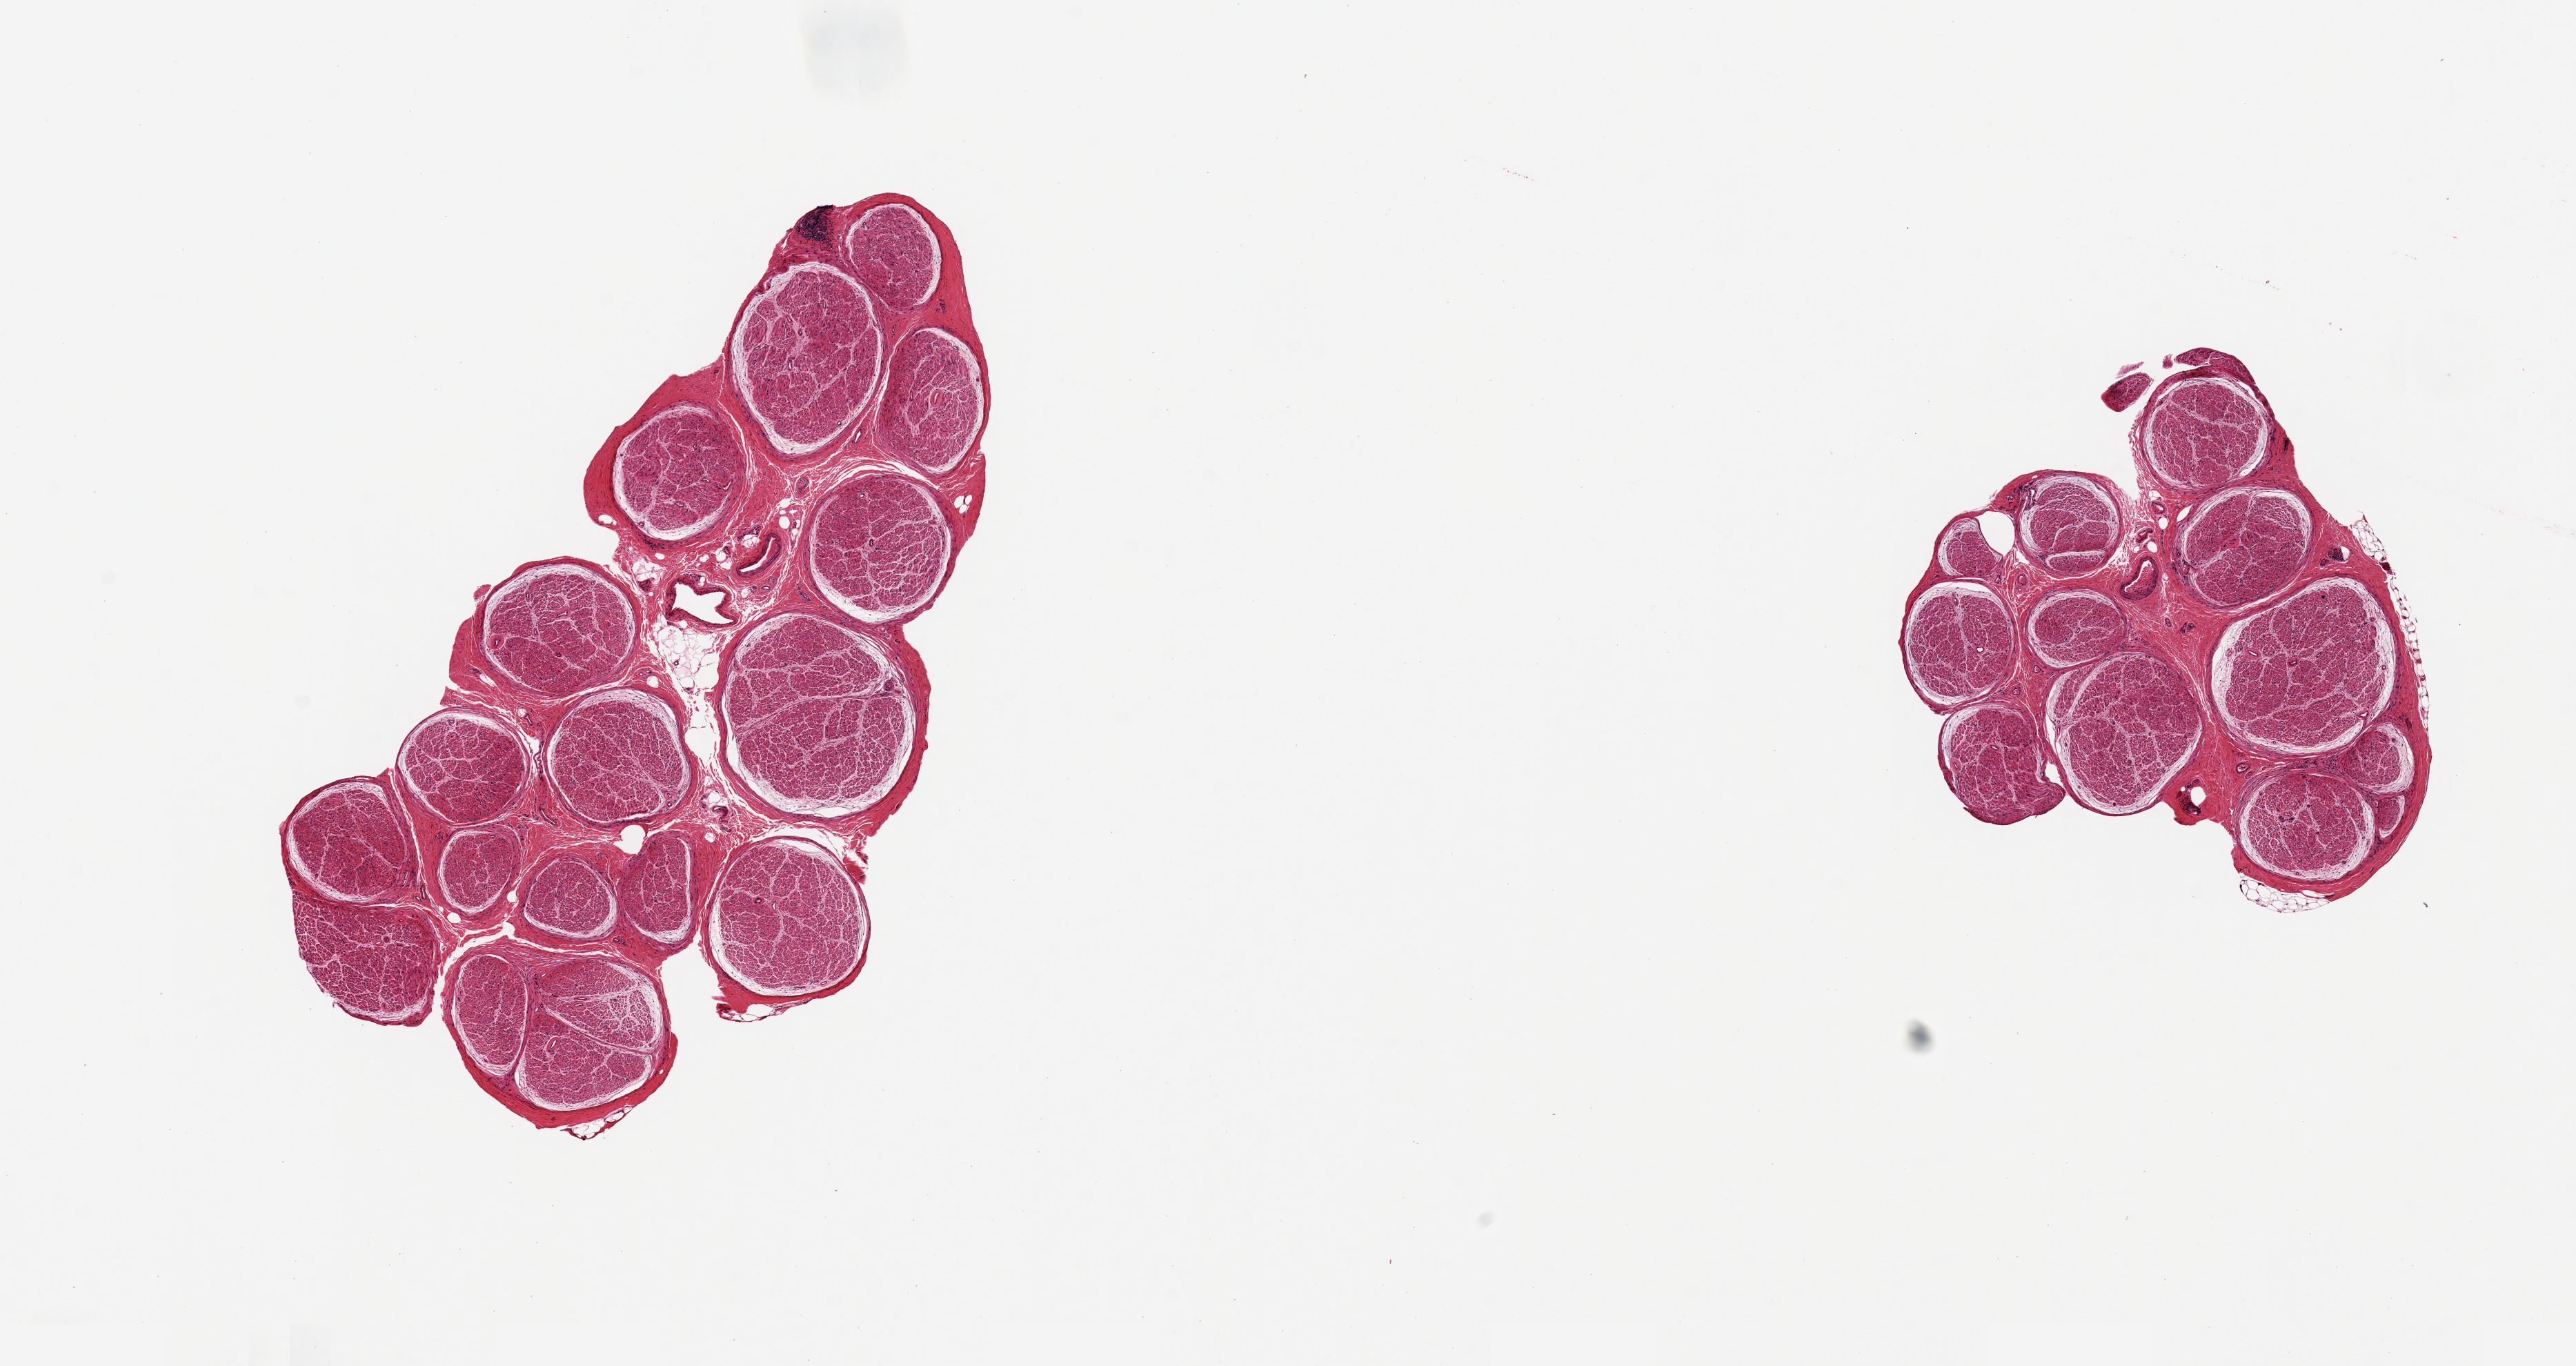
Digitized hematoxylin and eosin (H&E)-stained section — shown as a low-resolution overview of the whole scanned area (about 14.8 x 7.8 mm, from a 20x scan); PAXgene-fixed paraffin-embedded (PFPE) section; target tissue: tibial nerve; donor tissue sample.
• review note (as recorded): 2 pieces; well trimmed; minimal internal fat